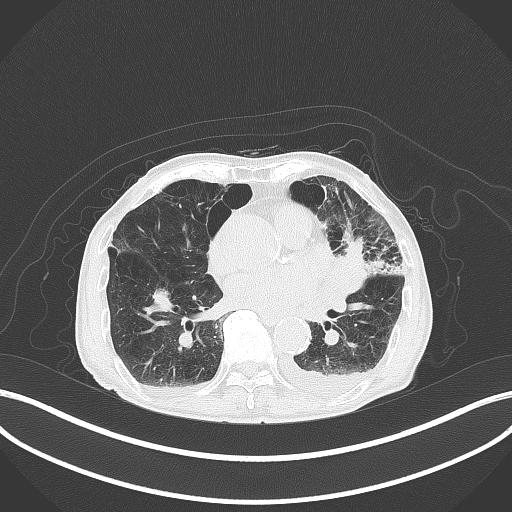
Chest CT, one axial slice; slice 180 of 227 in the series (ordered by position); reconstruction kernel B70f; 120 kVp; lung window (W 1500 / L -600 HU); 512 × 512 image matrix, field of view 400 × 400 mm. Patient: male, 90 years or older. From the clinical record (not read from this slice): clinical TNM (as recorded): T2b N1 M0.
Structures marked on this image (bounding box drawn by a radiologist):
- lung tumour (recorded histology: squamous cell carcinoma): bounding box (x1, y1, x2, y2) in pixels: (326, 235, 368, 300)